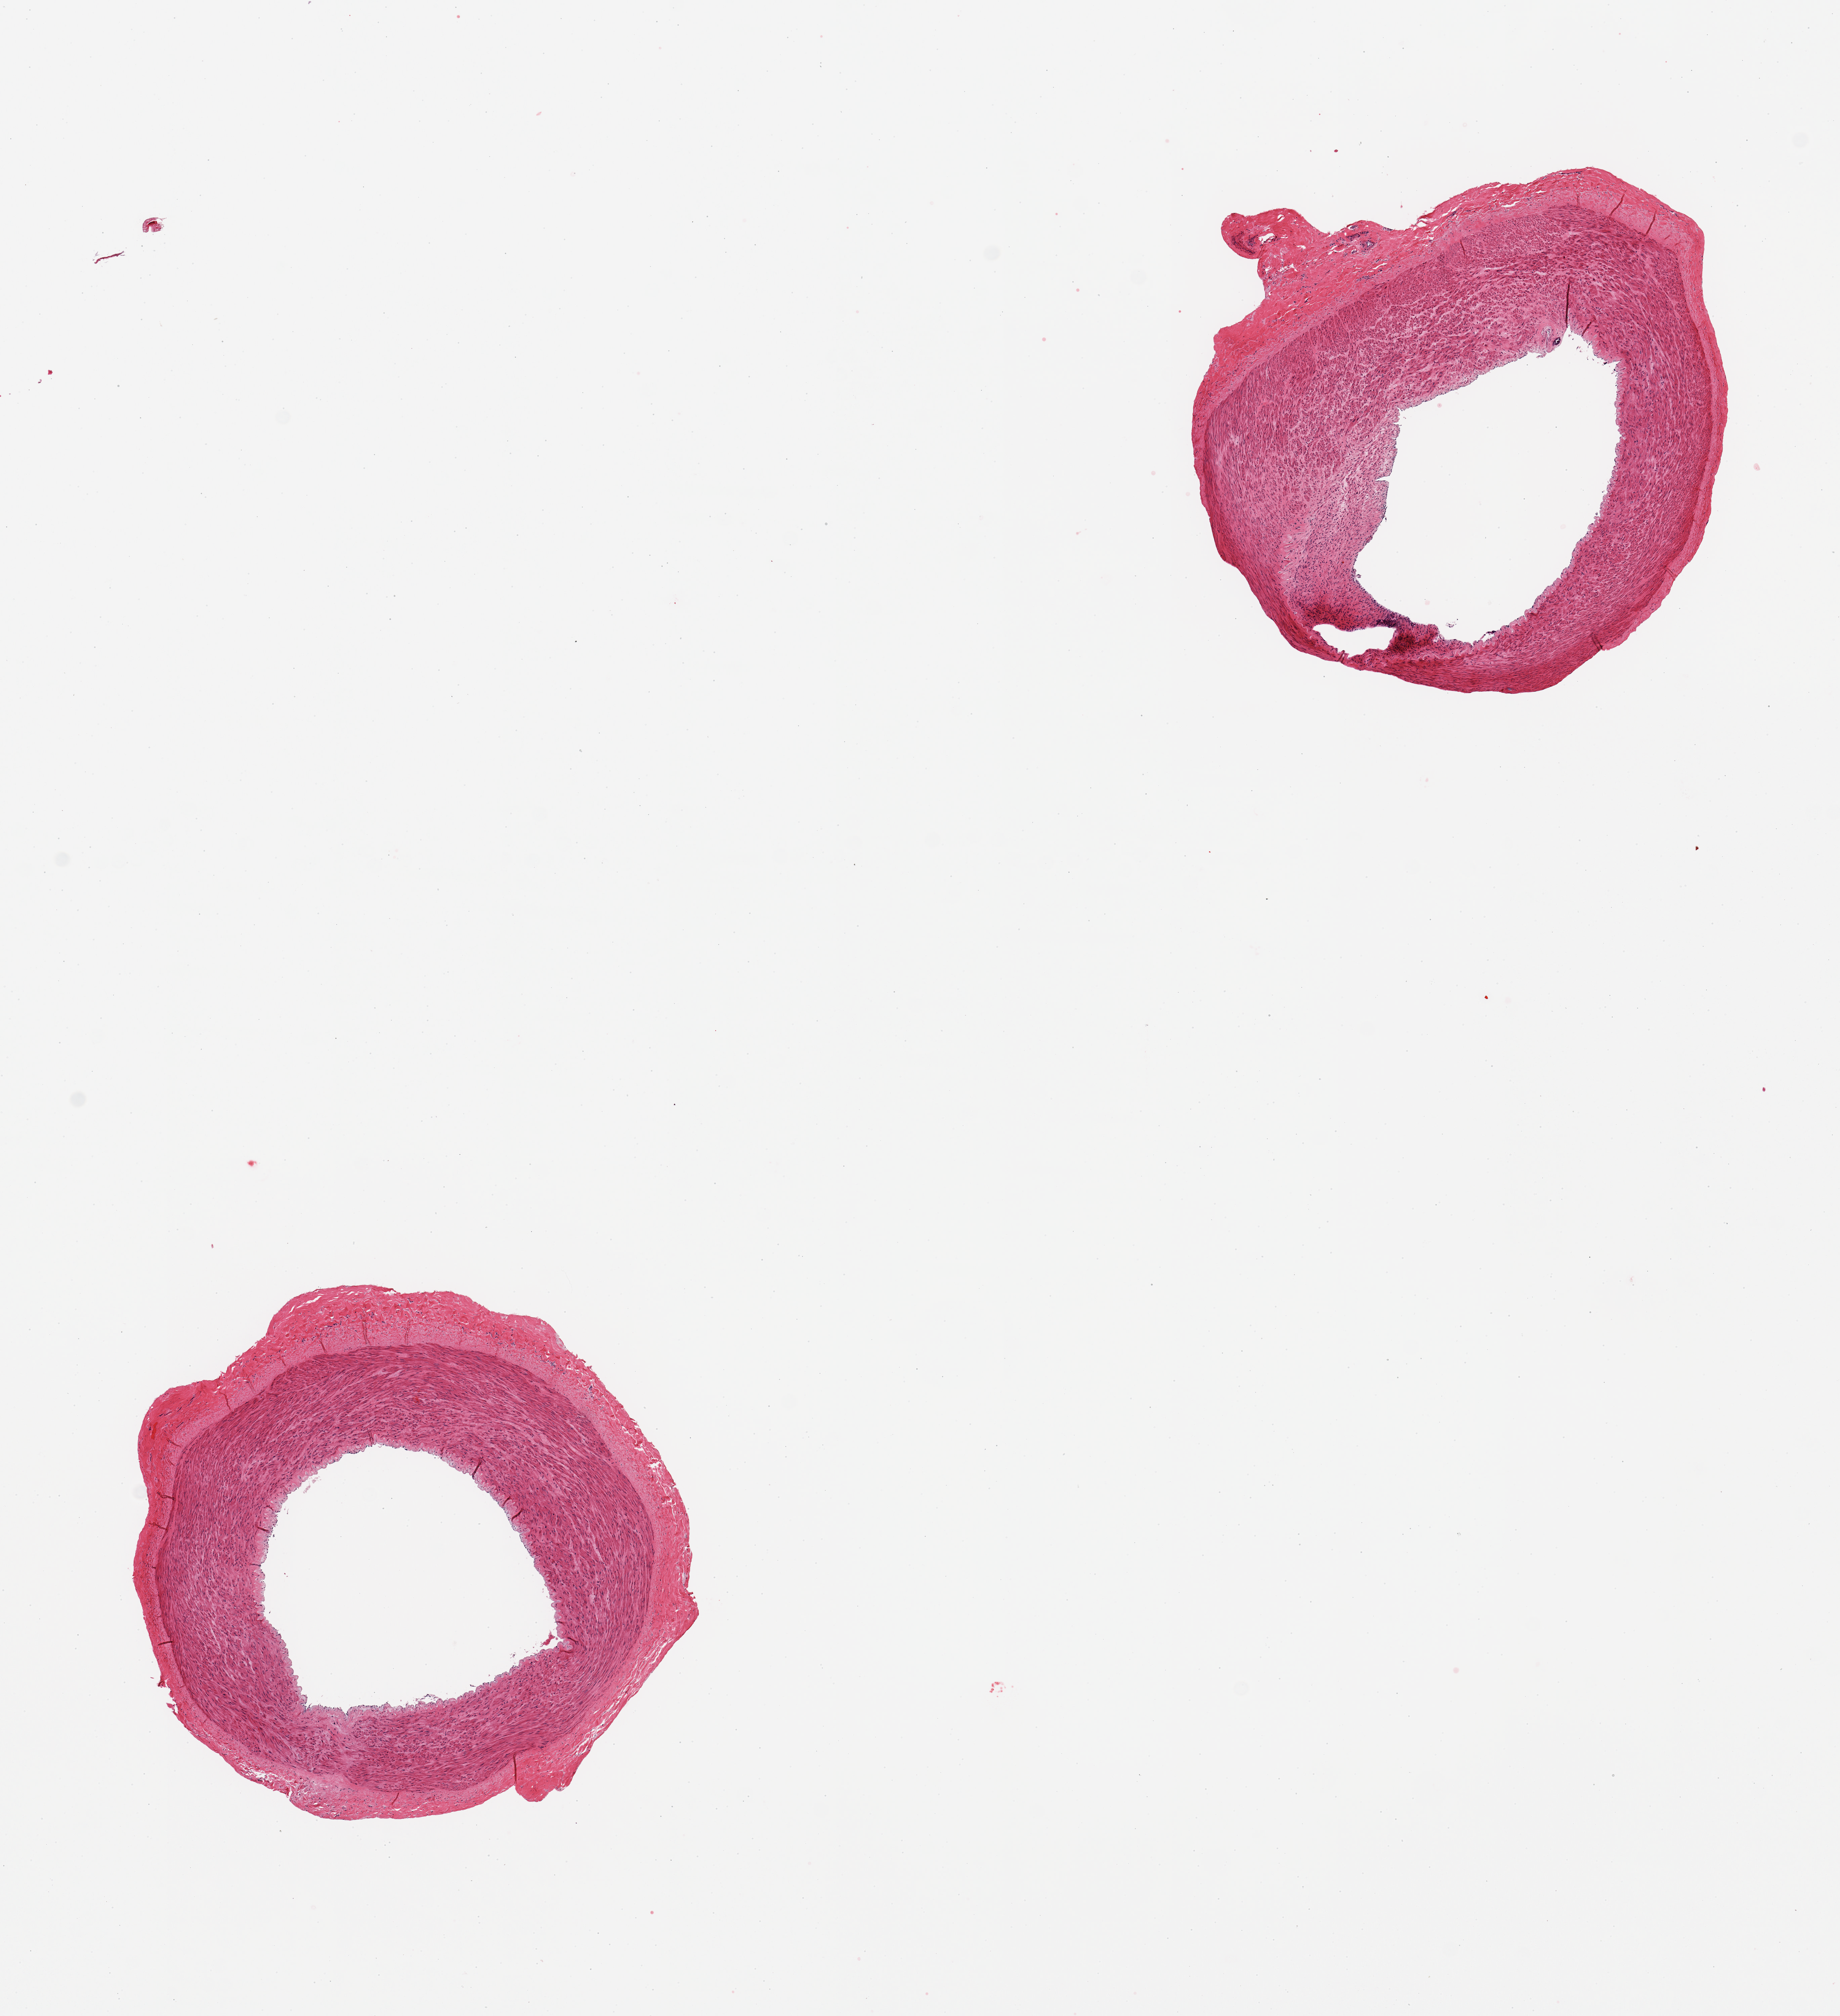
Hematoxylin and eosin (H&E) whole-slide image, a low-resolution overview of the entire scanned area, about 10.8 x 11.9 mm; PAXgene-fixed, paraffin-embedded tissue; sampled site (target tissue): tibial artery; donor tissue sample. Donor: male.
Reviewer comment on this tissue sample: 2 pieces; well trimmed.